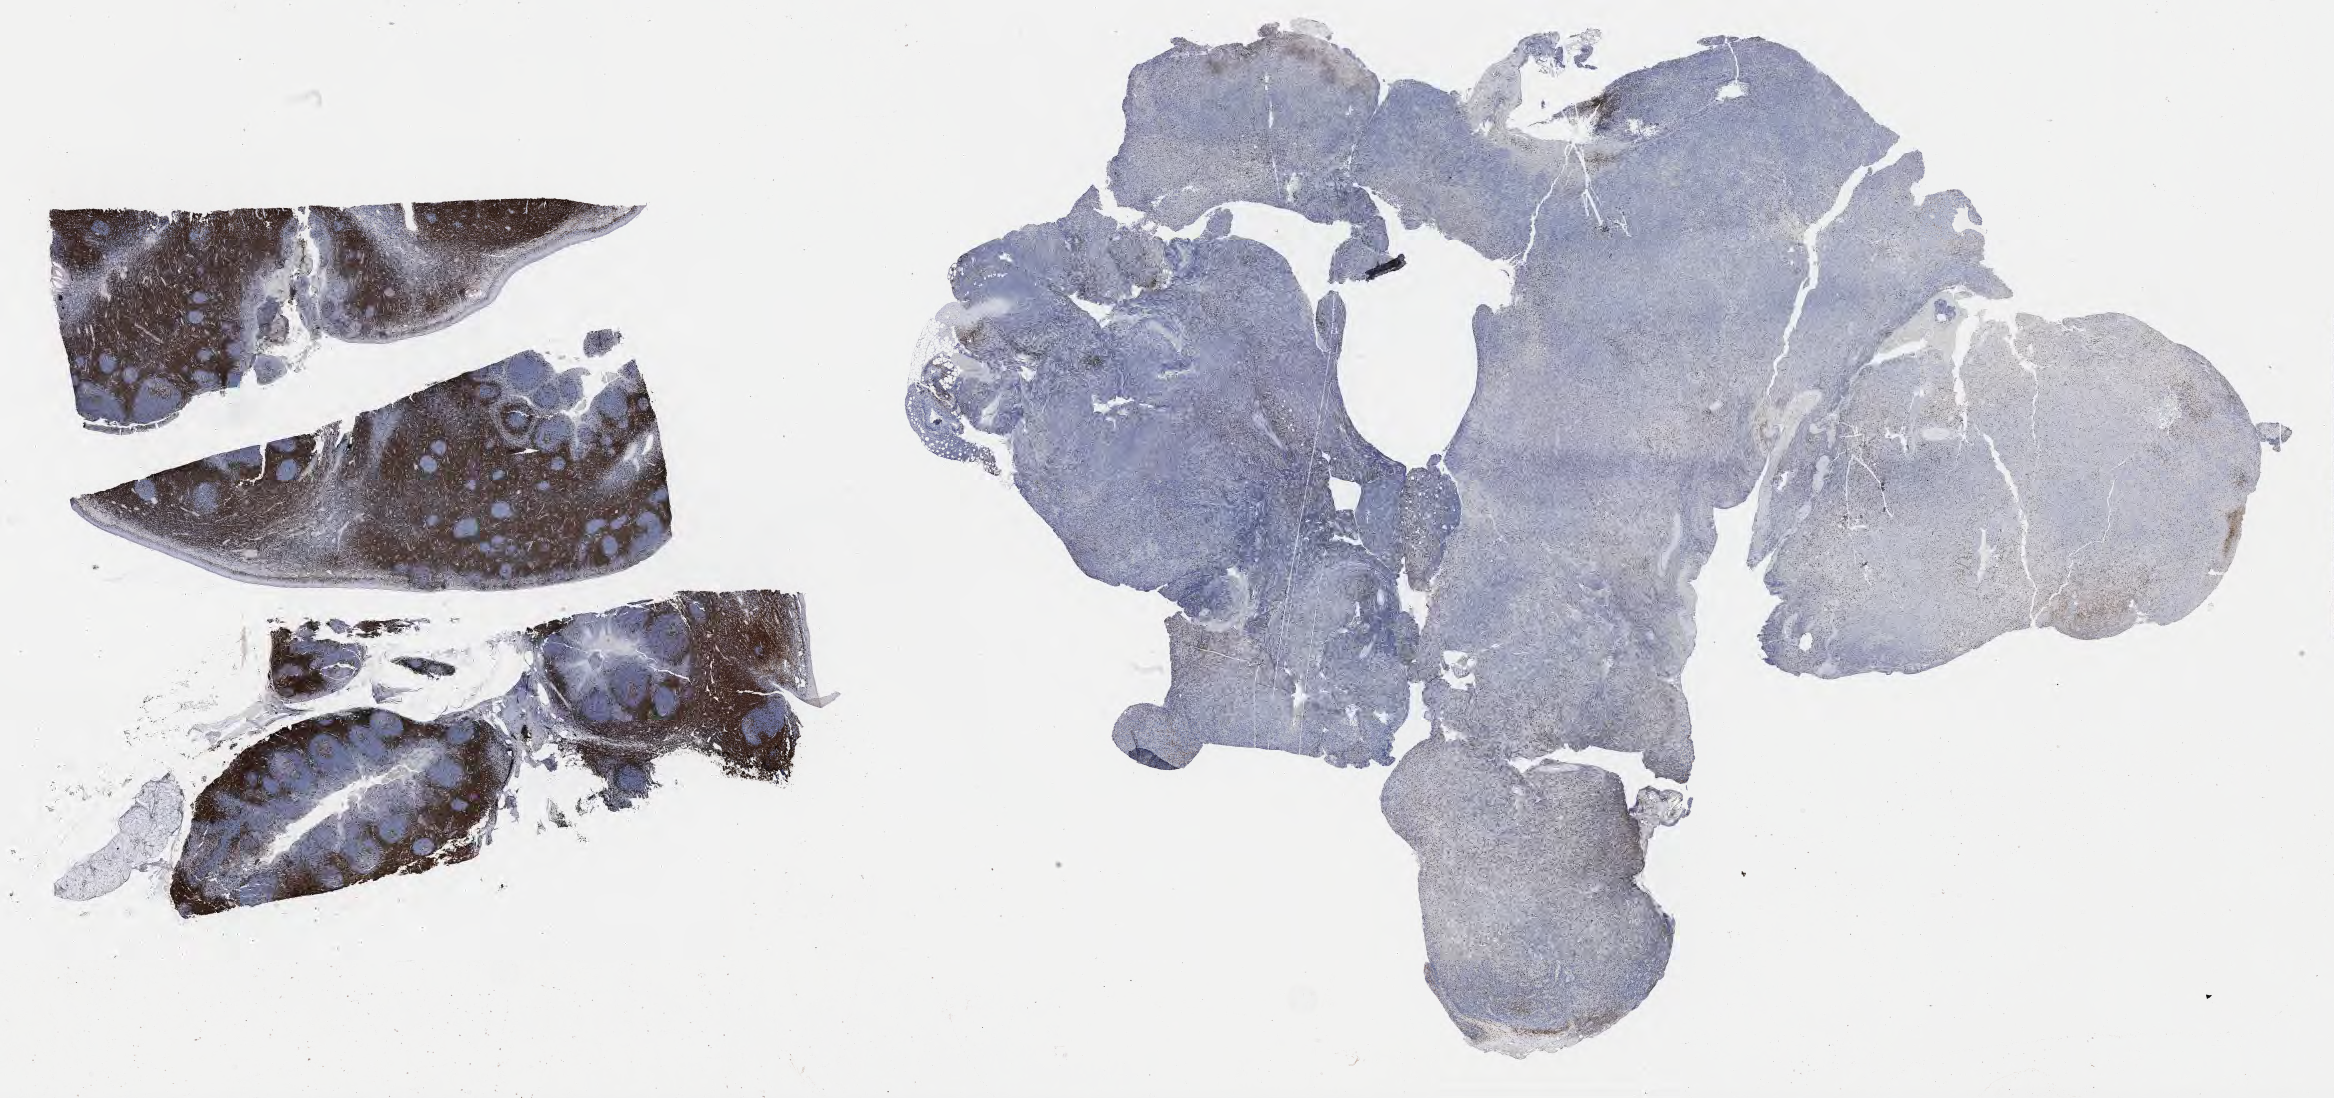
Immunohistochemistry (IHC) whole-slide image stained for CD3 — whole scanned area (about 37.8 x 17.8 mm) shown as a low-resolution overview; specimen: tumor tissue; site: soft tissue of abdomen. Female patient; age at initial diagnosis 8 years.
Histologic diagnosis: Burkitt lymphoma, NOS.